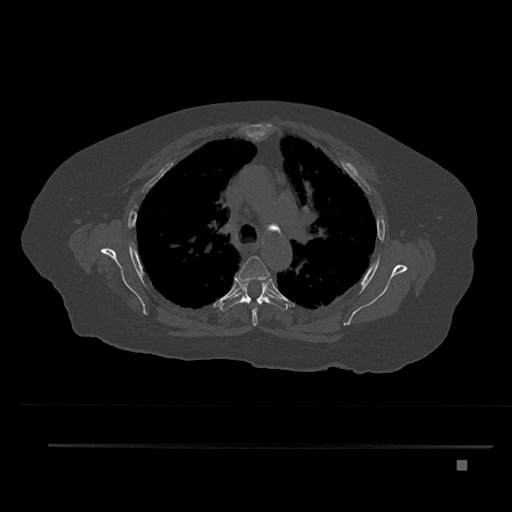
CT including the spine, one axial slice; slice 582 of 797 in the series (ordered by position); reconstruction kernel Br40s/3; 120 kVp; bone window (W 1800 / L 400 HU); 0.5 mm slice thickness; 512 × 512 image matrix, field of view 437 × 437 mm. Patient: female, 76 years. Case-level facts recorded for this patient, not image findings: primary cancer: lung; vertebrae with lytic lesions (as recorded): T11, L3.
Annotated regions visible in this slice (semi-automatic segmentation, software-assisted and operator-edited):
- T4 vertebra: bounding box (x1, y1, x2, y2) in pixels: (236, 255, 270, 326)
- T5 vertebra: (219, 279, 288, 311)